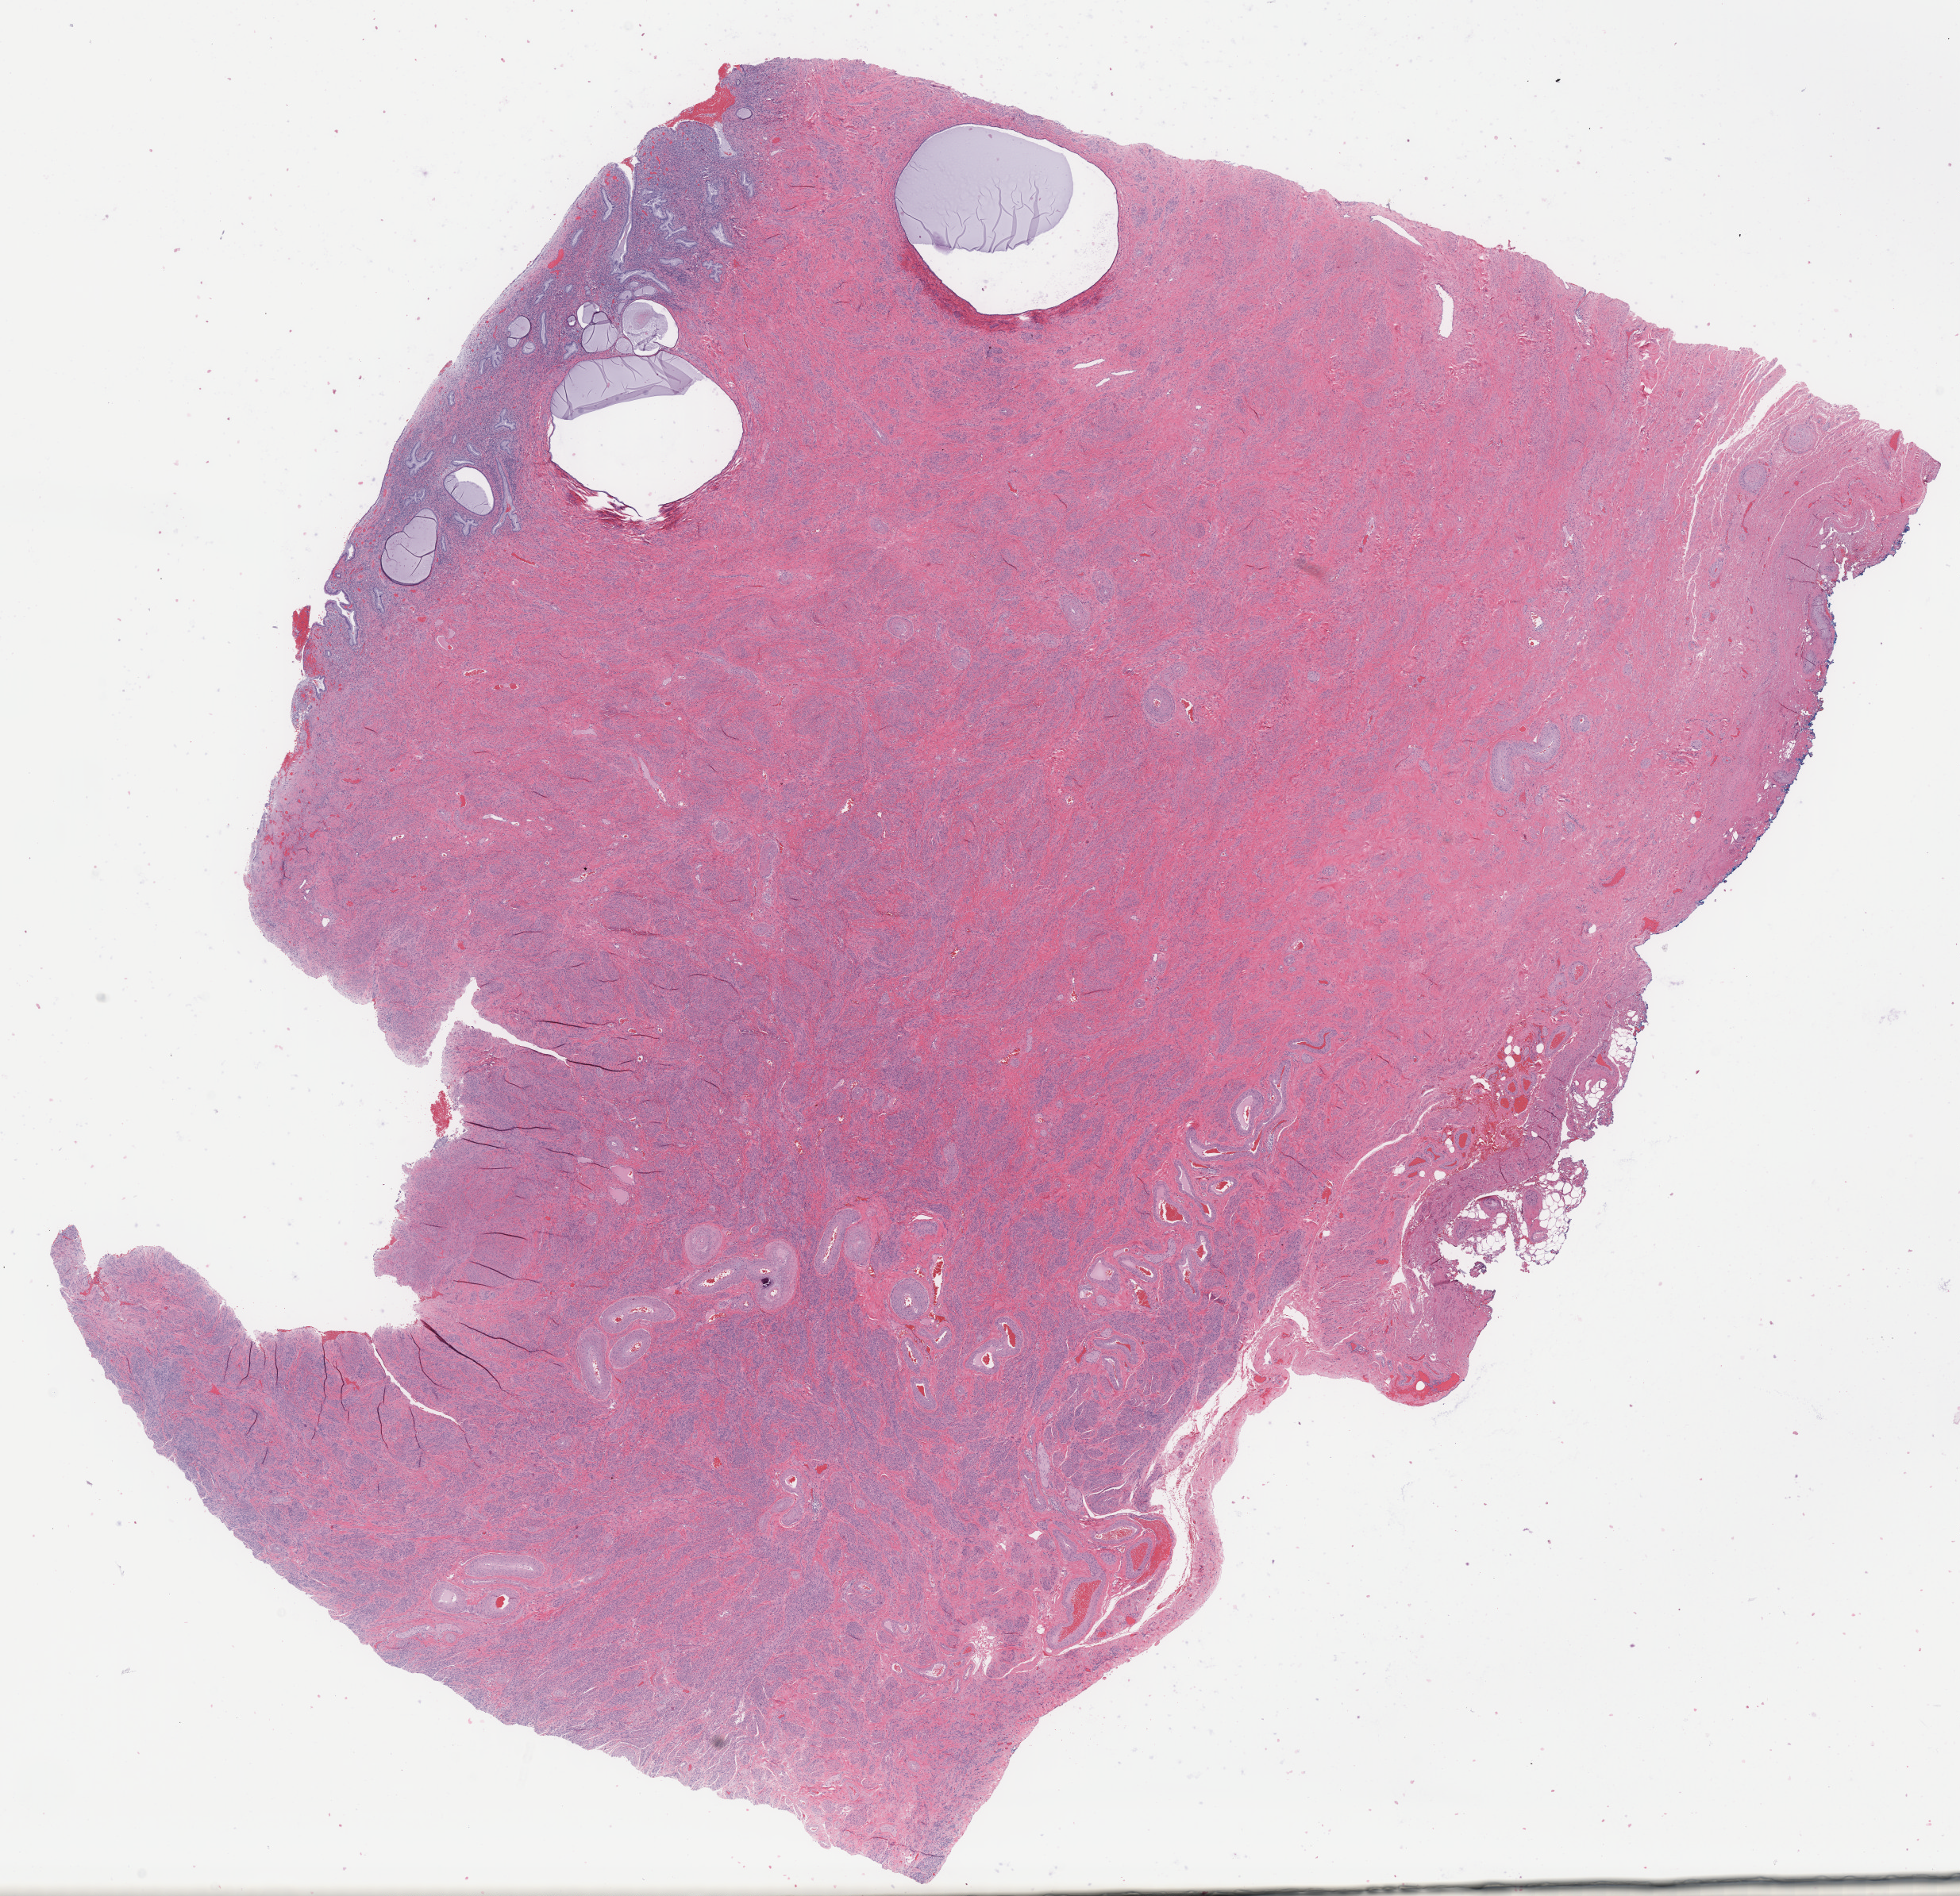
Haematoxylin and eosin whole-slide image, shown as a low-resolution overview of the whole scanned area (about 19.5 x 18.9 mm). Cryosection. Specimen: non-tumor (normal tissue) sample from a patient with serous carcinoma, NOS. Anatomic site: endometrium. Patient sex: female. Slide review estimates, as recorded: tumor cells 0%, tumor nuclei 0%, stromal cells 90%, necrosis 0%, normal cells 10%. Inflammatory infiltration, as recorded: lymphocyte infiltration 6%, monocyte infiltration 3%, neutrophil infiltration 7%.
This section: non-tumor tissue sample; the patient's diagnosis is given above.